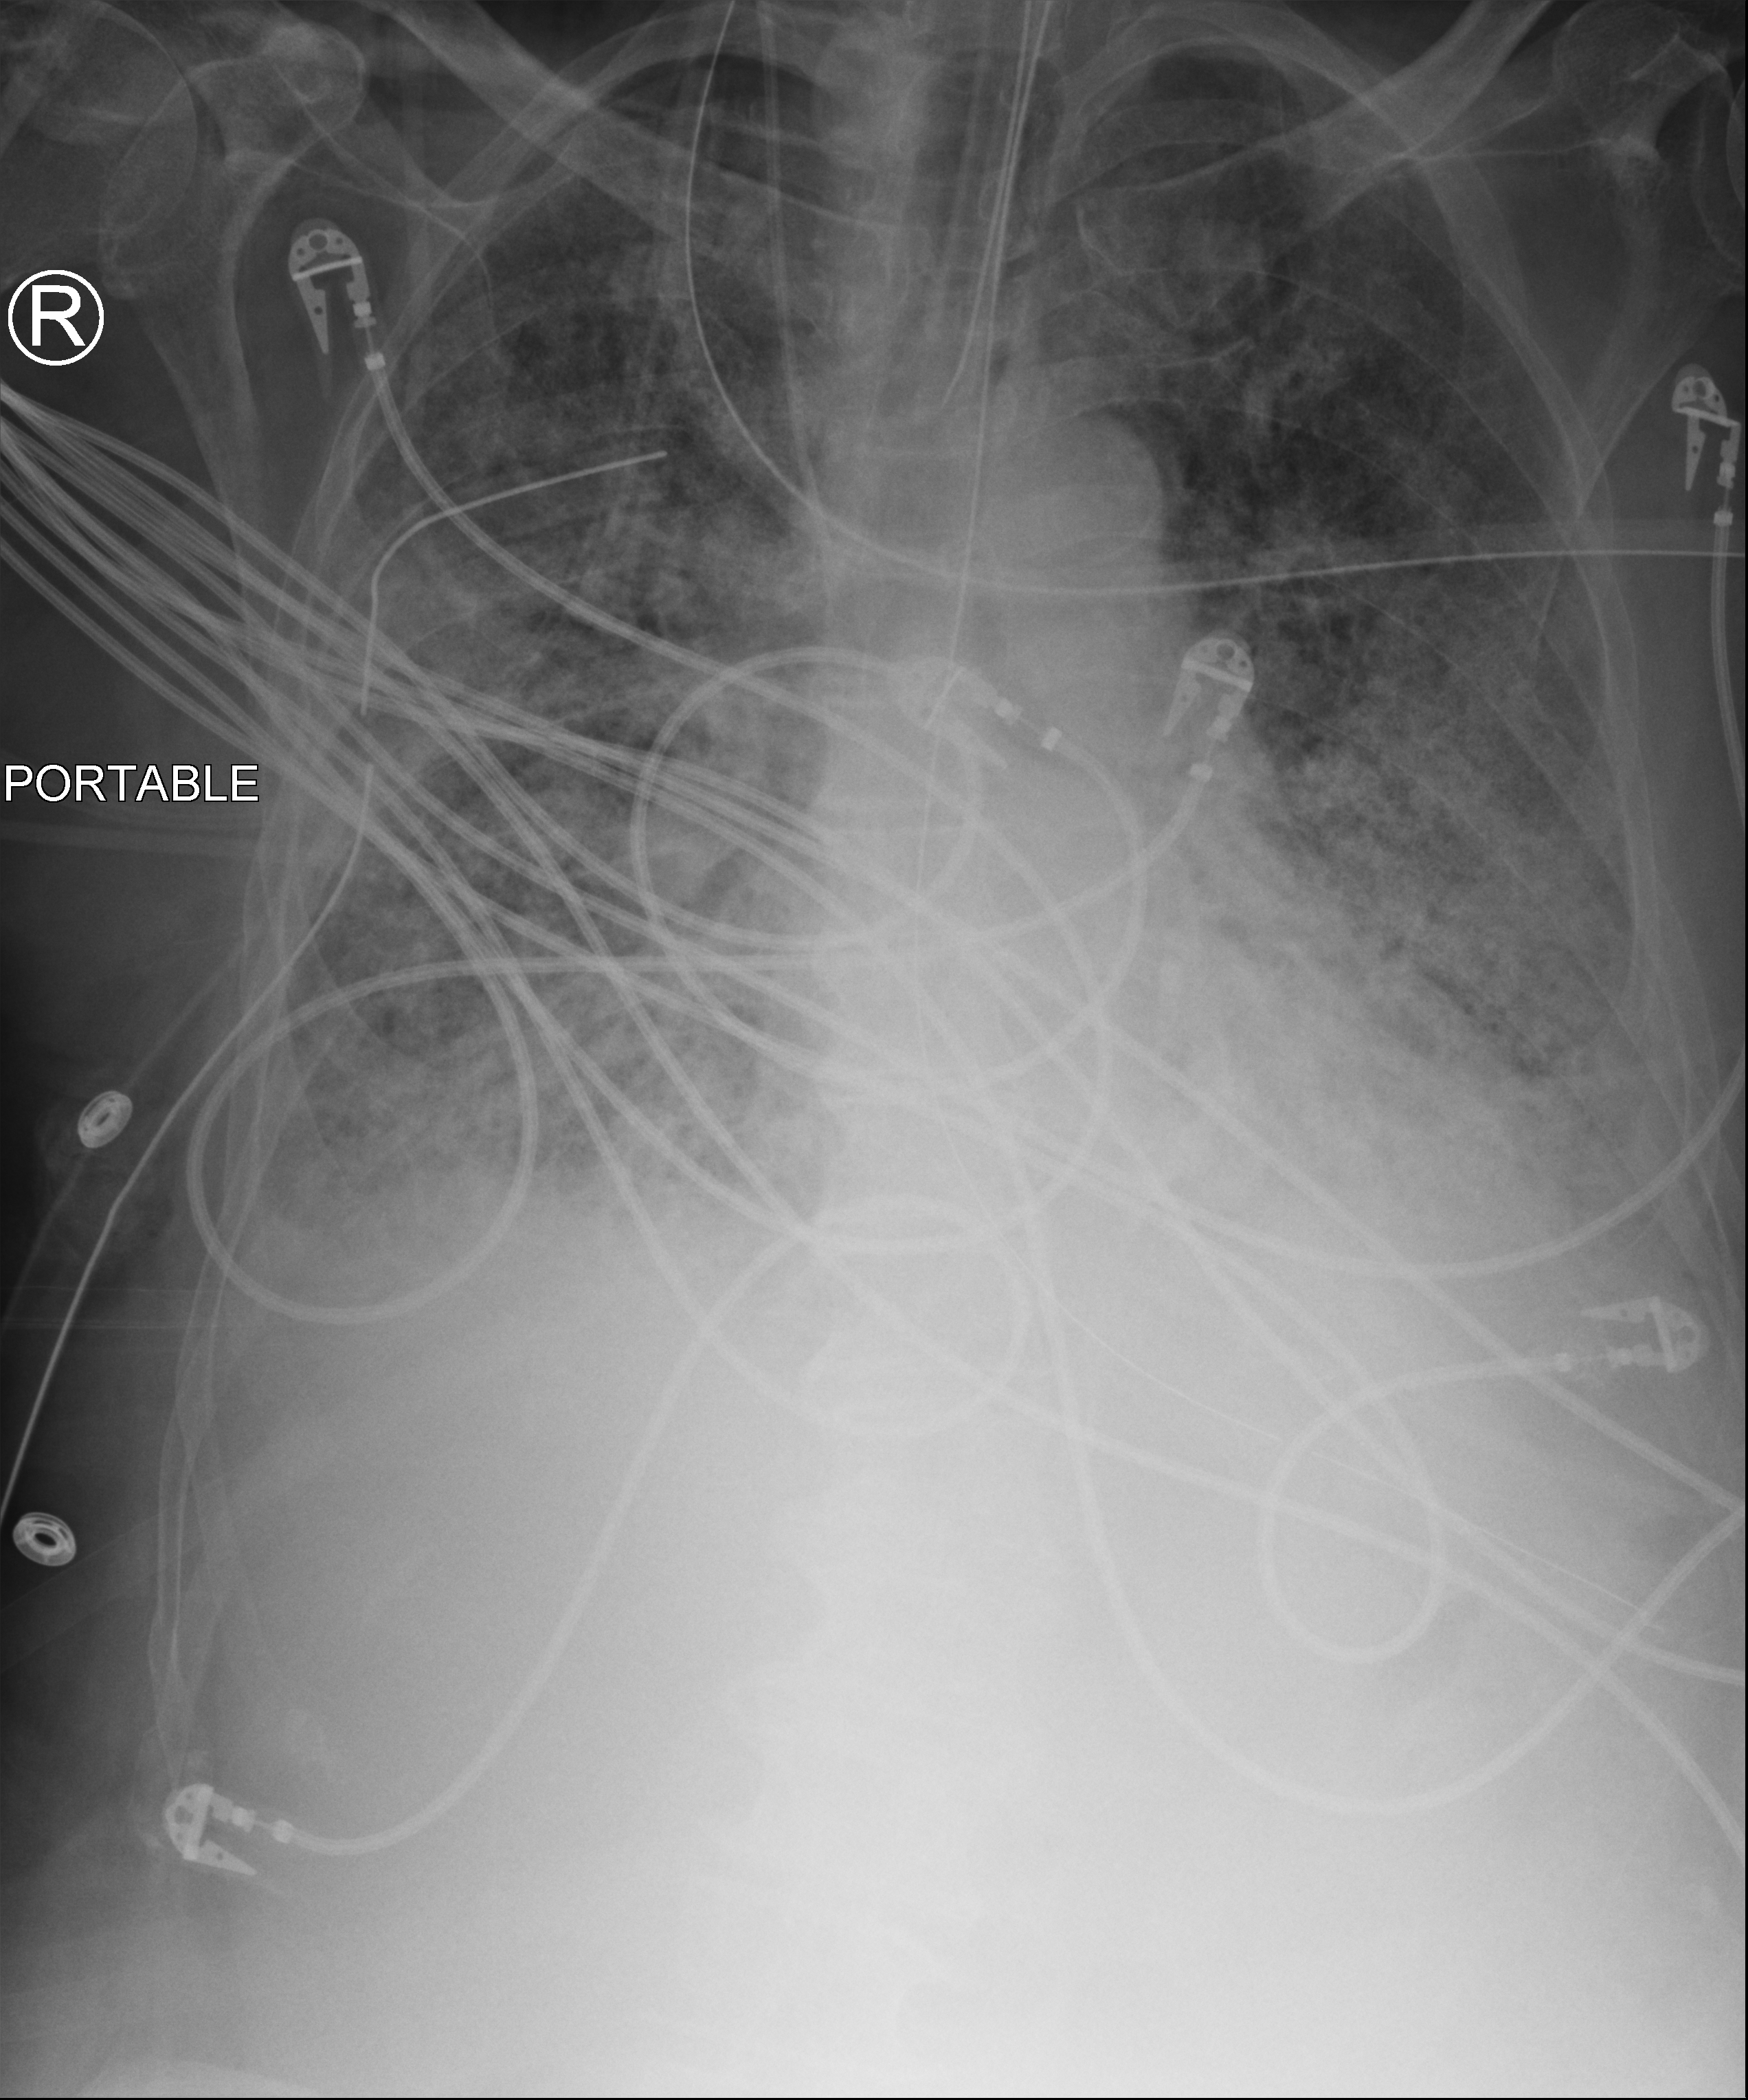
Bedside chest radiograph (computed radiography), anteroposterior (AP) projection. Male patient hospitalised with COVID-19, age 75–90 years.
From the hospital-stay record, not from the radiograph (when in the stay this image was taken is not recorded): length of hospital stay: 47 days; admitted to intensive care during this hospital stay: yes.